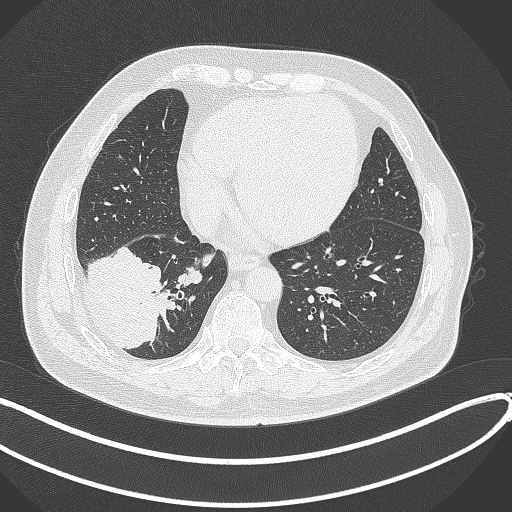
Chest CT, one axial slice; position 115 of 360 along the scan axis; 120 kVp; lung window (W 1500 / L -600 HU); 512 × 512 image matrix. Male patient, age 59 years.
Outlined on this slice (rectangle marked by the reading radiologist):
- lung tumour (recorded histology: adenocarcinoma): box from (x=84, y=245) to (x=180, y=348) px